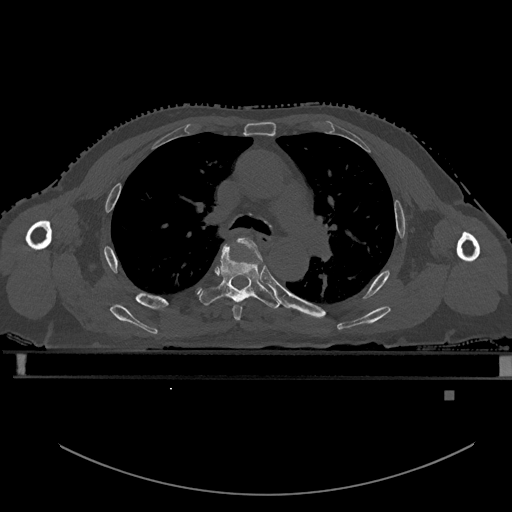
CT including the spine, one axial slice; slice 371 of 969 in the series (ordered by position); bone window (W 1800 / L 400 HU); 0.5 mm slice thickness; 512 × 512 image matrix. Male patient, age 82 years. Case-level facts recorded for this patient, not image findings: primary cancer: prostate; vertebrae with lytic lesions (as recorded): T11, T9, T8, T2.
Outlined on this slice (semi-automatic segmentation, software-assisted and operator-edited):
- T4 vertebra: bounding box <233,238,261,321> (left, top, right, bottom; pixels)
- T5 vertebra: <200,245,280,309>